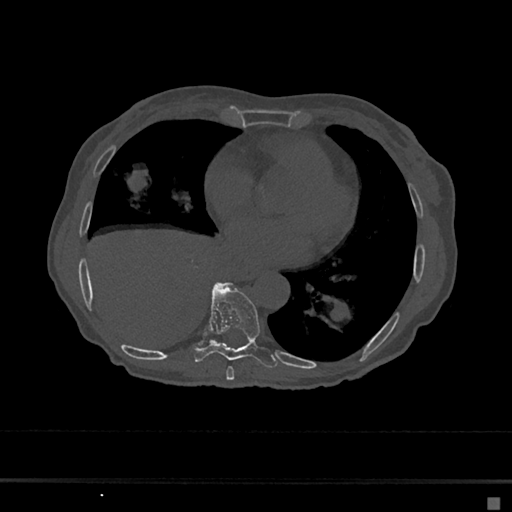
CT including the spine, one axial slice. Slice 323 of 797 in the series (ordered by position). Reconstruction kernel Br40s/3. Bone window (W 1800 / L 400 HU). 0.5 mm slice thickness. 512 × 512 image matrix. Female patient, age 68 years. From the clinical record (not read from this slice): primary cancer: renal.
Structures marked on this image (semi-automatically segmented with operator editing):
- T7 vertebra: bounding box (x1, y1, x2, y2) in pixels: (226, 366, 235, 381)
- T8 vertebra: (193, 282, 278, 368)
- T9 vertebra: (218, 283, 224, 285)